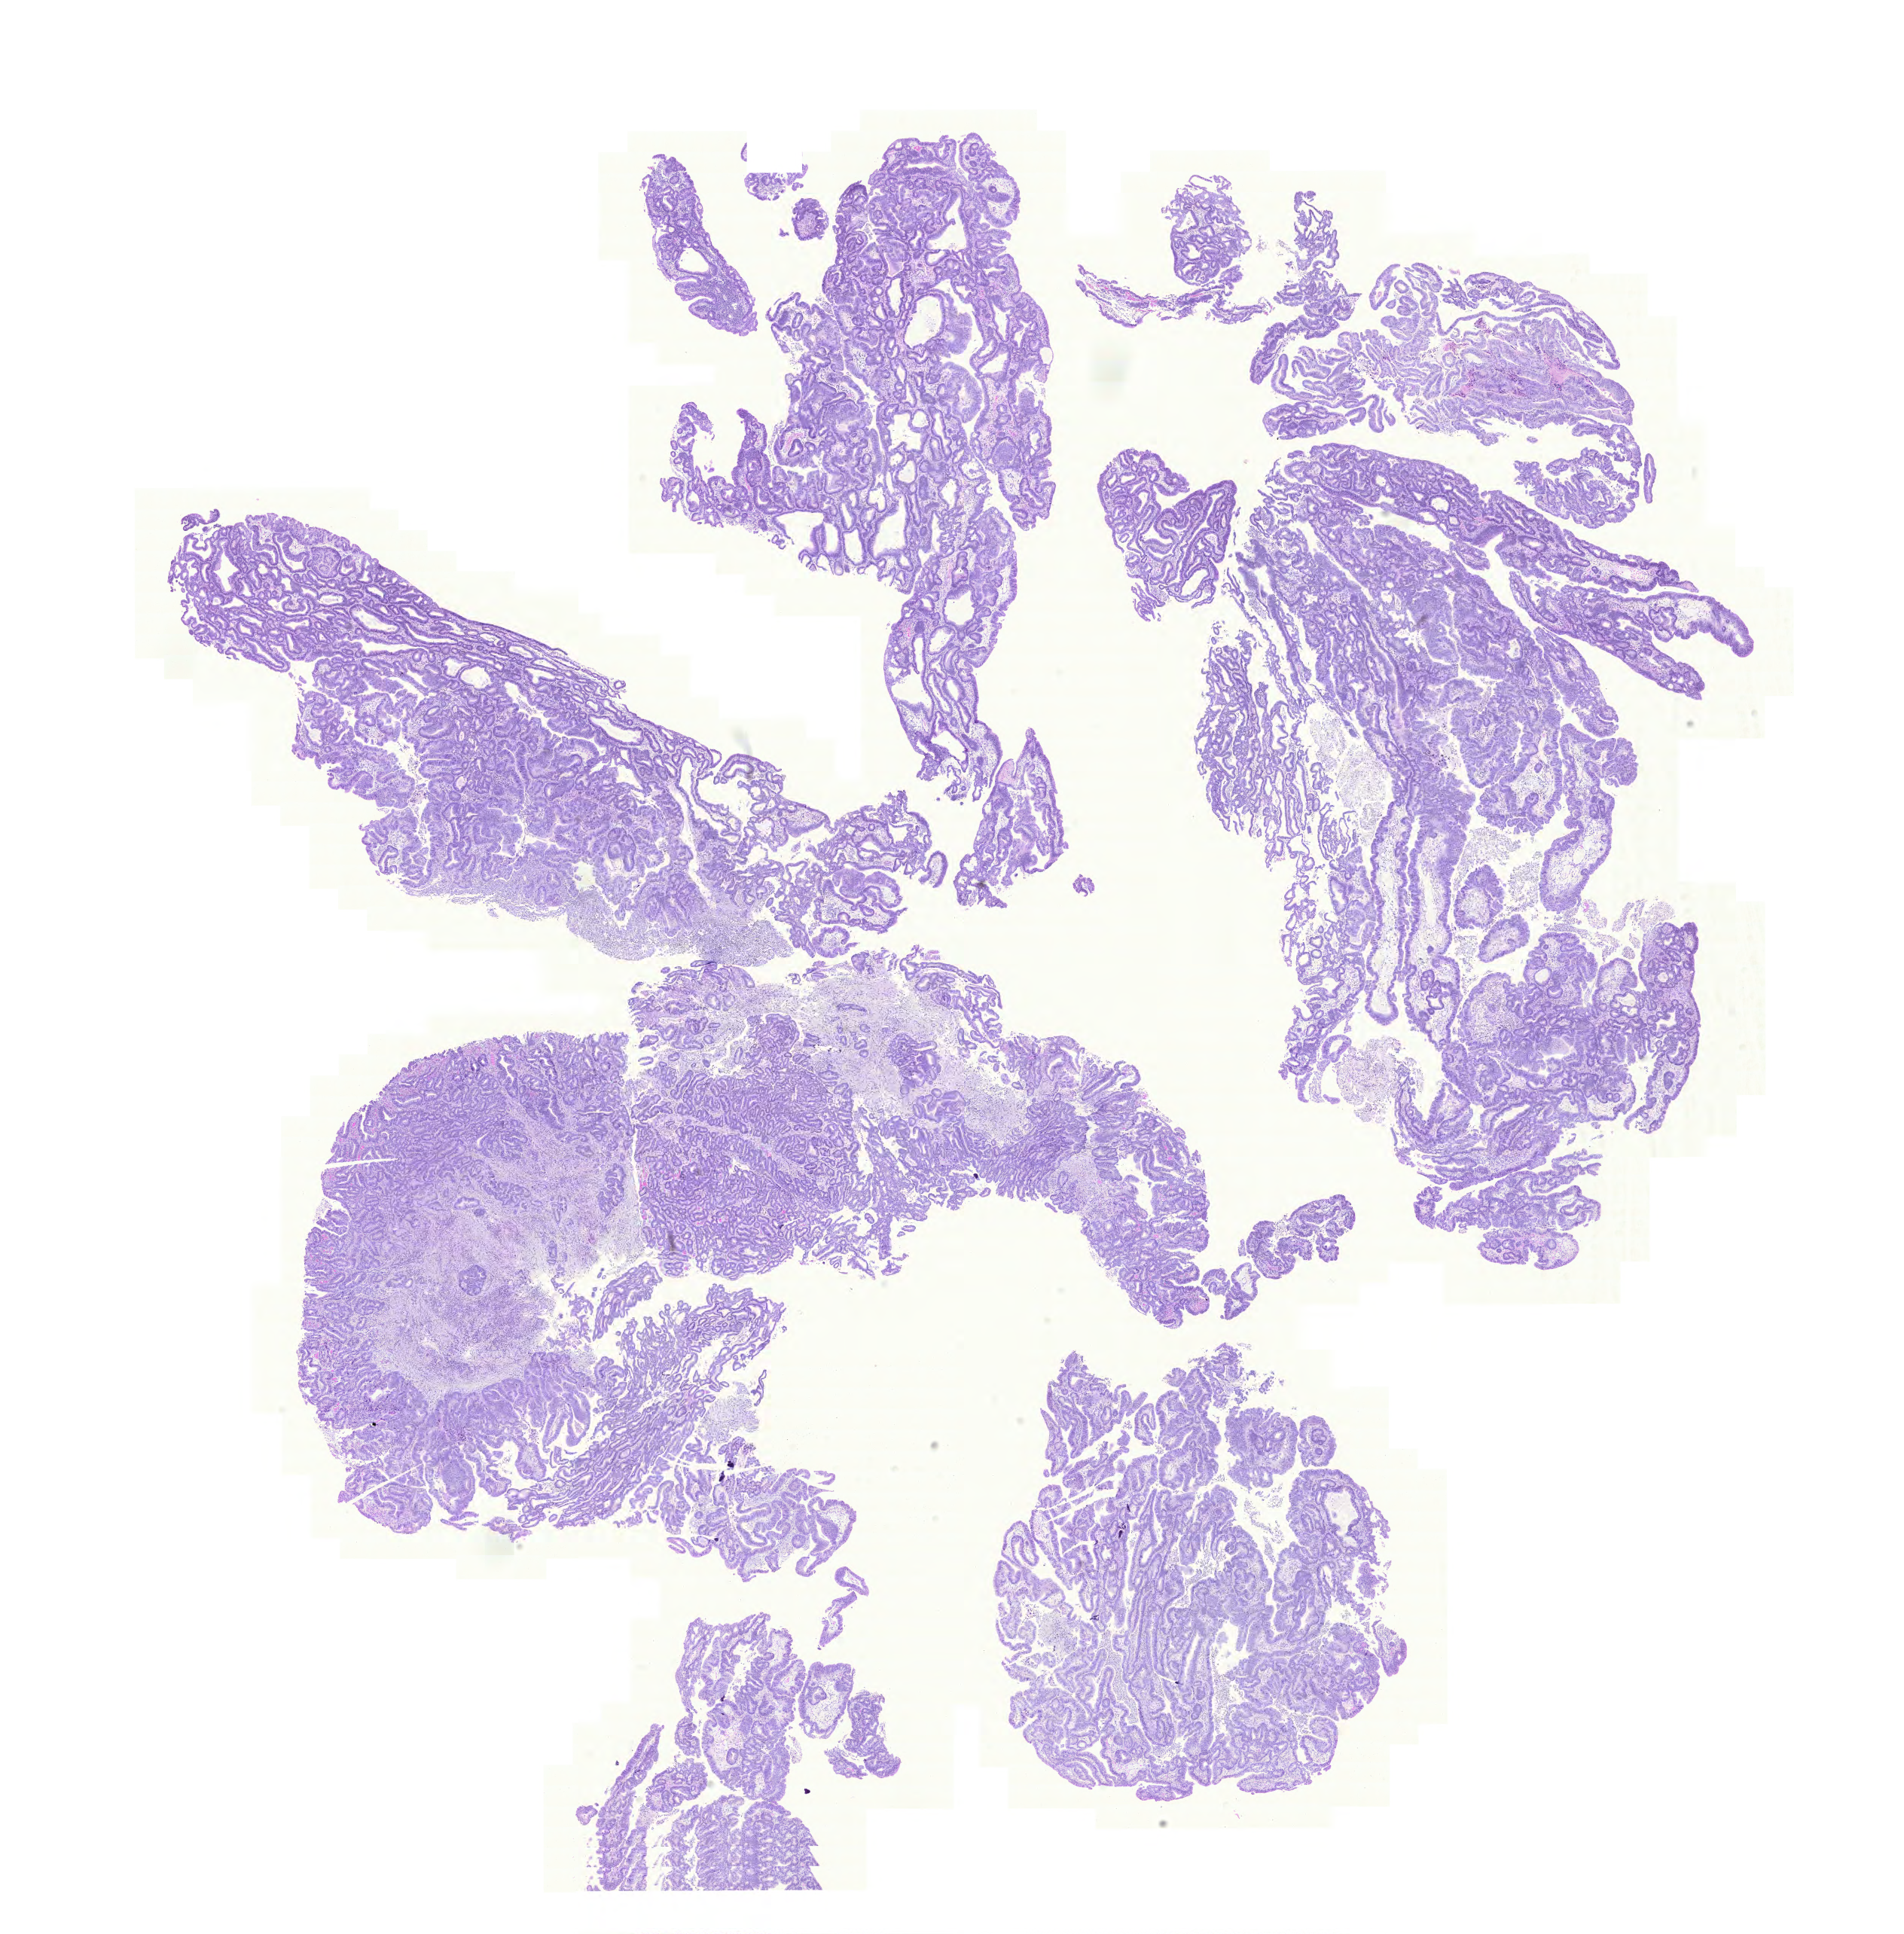
Whole-slide histology image, H&E, a low-resolution overview of the entire scanned area, about 18.8 x 19.1 mm. FFPE section. Sample: primary tumour, stomach. Male, age 84 years at initial diagnosis. Histologic grade: G2 (moderately differentiated).
Histologic diagnosis: Adenocarcinoma, NOS (cardia, NOS). AJCC pathologic stage: IB (6th edition).